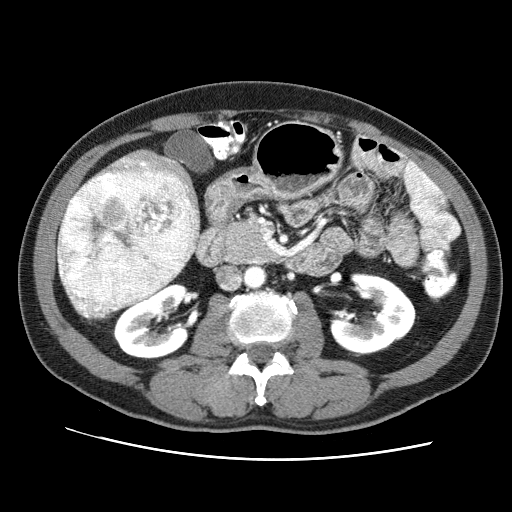
Contrast-enhanced abdominal CT (liver protocol), one axial slice; slice 26 of 71 in the series (ordered by position); reconstruction kernel STANDARD; 120 kVp; soft-tissue window (W 400 / L 40 HU); 2.5 mm slice thickness; 512 × 512 image matrix, field of view 360 × 360 mm. From the clinical record (not read from this slice): diagnosis: hepatocellular carcinoma (patient treated with transarterial chemoembolisation; whether this scan precedes or follows treatment is not stated here); TNM stage (as recorded): Stage-II; Child-Pugh class: A; tumour differentiation: well differentiated; tumour nodularity: multinodular.
Structures marked on this image (semi-automatic segmentation, software-assisted and operator-edited):
- liver parenchyma outside the tumour (the mass and vessels are separate outlines, so this box may not span the whole liver): bounding box <57,148,200,311> (left, top, right, bottom; pixels)
- mass: <57,168,200,318>
- liver vessels: <121,159,183,268>